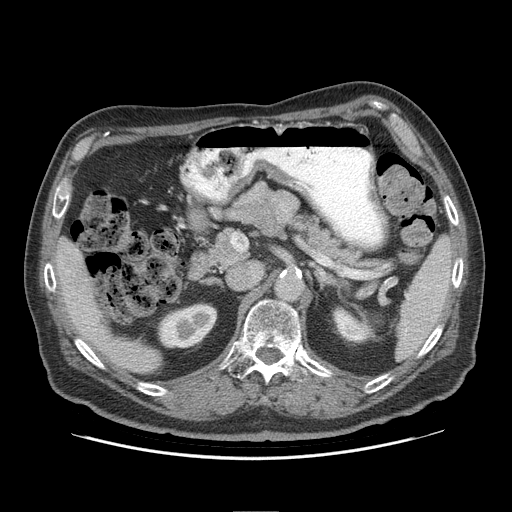
Contrast-enhanced abdominal CT (liver protocol), one axial slice. Position 50 of 95 along the scan axis. Reconstruction kernel STANDARD. 140 kVp. Soft-tissue window (W 400 / L 40 HU). 2.5 mm slice thickness. 512 × 512 image matrix. Case-level facts recorded for this patient, not image findings: diagnosis: hepatocellular carcinoma (patient treated with transarterial chemoembolisation; whether this scan precedes or follows treatment is not stated here); TNM stage (as recorded): Stage-IVB; Child-Pugh class: A; tumour differentiation: well differentiated; tumour nodularity: uninodular.
Annotated regions visible in this slice (semi-automatically segmented with operator editing):
- liver parenchyma outside the tumour (the mass and vessels are separate outlines, so this box may not span the whole liver): bounding box [x1, y1, x2, y2] px = [54, 237, 158, 372]